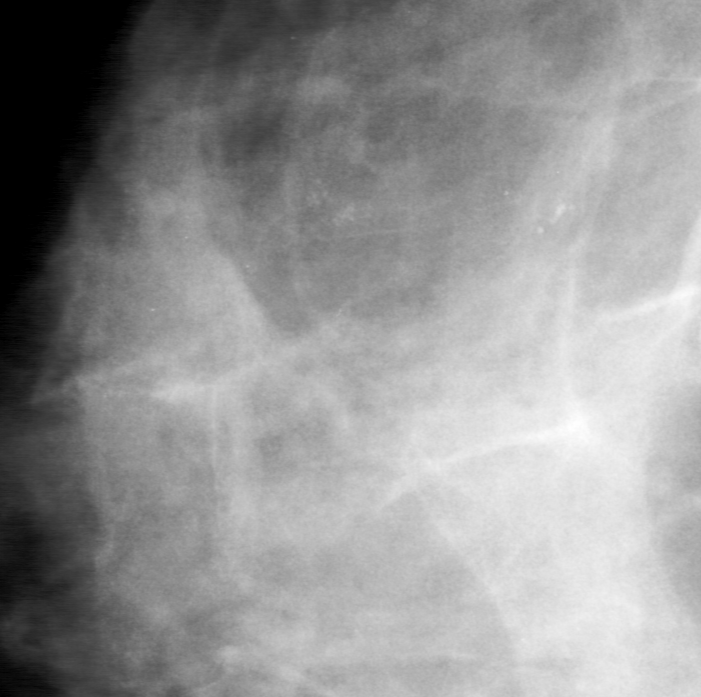
Region of interest cut from a scanned film mammogram (one marked finding), right breast, CC view, BI-RADS breast density category 2 (scale 1–4).
Marked abnormality: calcifications, morphology amorphous, distribution clustered; BI-RADS assessment category 0 (incomplete: needs additional imaging); pathology (as recorded): benign.